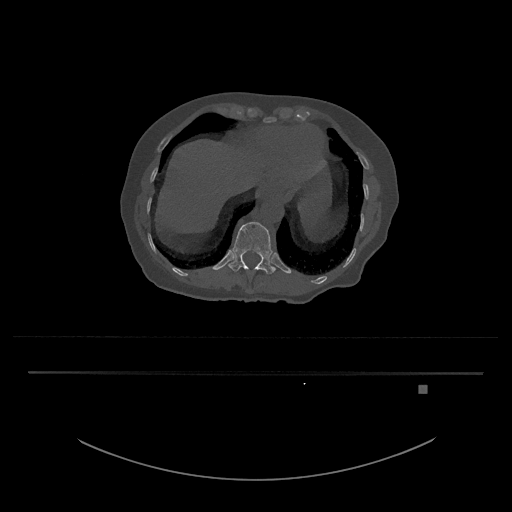
CT including the spine, one axial slice. Slice 623 of 797 in the series (ordered by position). Reconstruction kernel Br40s/3. 120 kVp. Bone window (W 1800 / L 400 HU). 0.5 mm slice thickness. 512 × 512 image matrix. Patient: female, 57 years. Case-level facts recorded for this patient, not image findings: primary cancer: cervical.
Structures marked on this image (semi-automatic segmentation, software-assisted and operator-edited):
- T12 vertebra: bounding box [x1, y1, x2, y2] px = [228, 222, 276, 274]